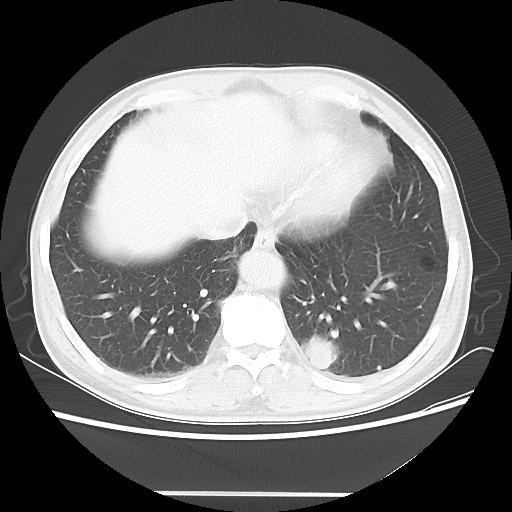
Chest CT, one axial slice. Position 14 of 60 along the scan axis. 100 kVp. Lung window (W 1500 / L -600 HU). 512 × 512 image matrix, field of view 360 × 360 mm. Male patient, age 55 years. Case-level facts recorded for this patient, not image findings: clinical TNM (as recorded): T1c N3 M0.
Annotated regions visible in this slice (rectangle marked by the reading radiologist):
- lung tumour (recorded histology: small cell carcinoma): bounding box [x1, y1, x2, y2] px = [297, 328, 342, 377]